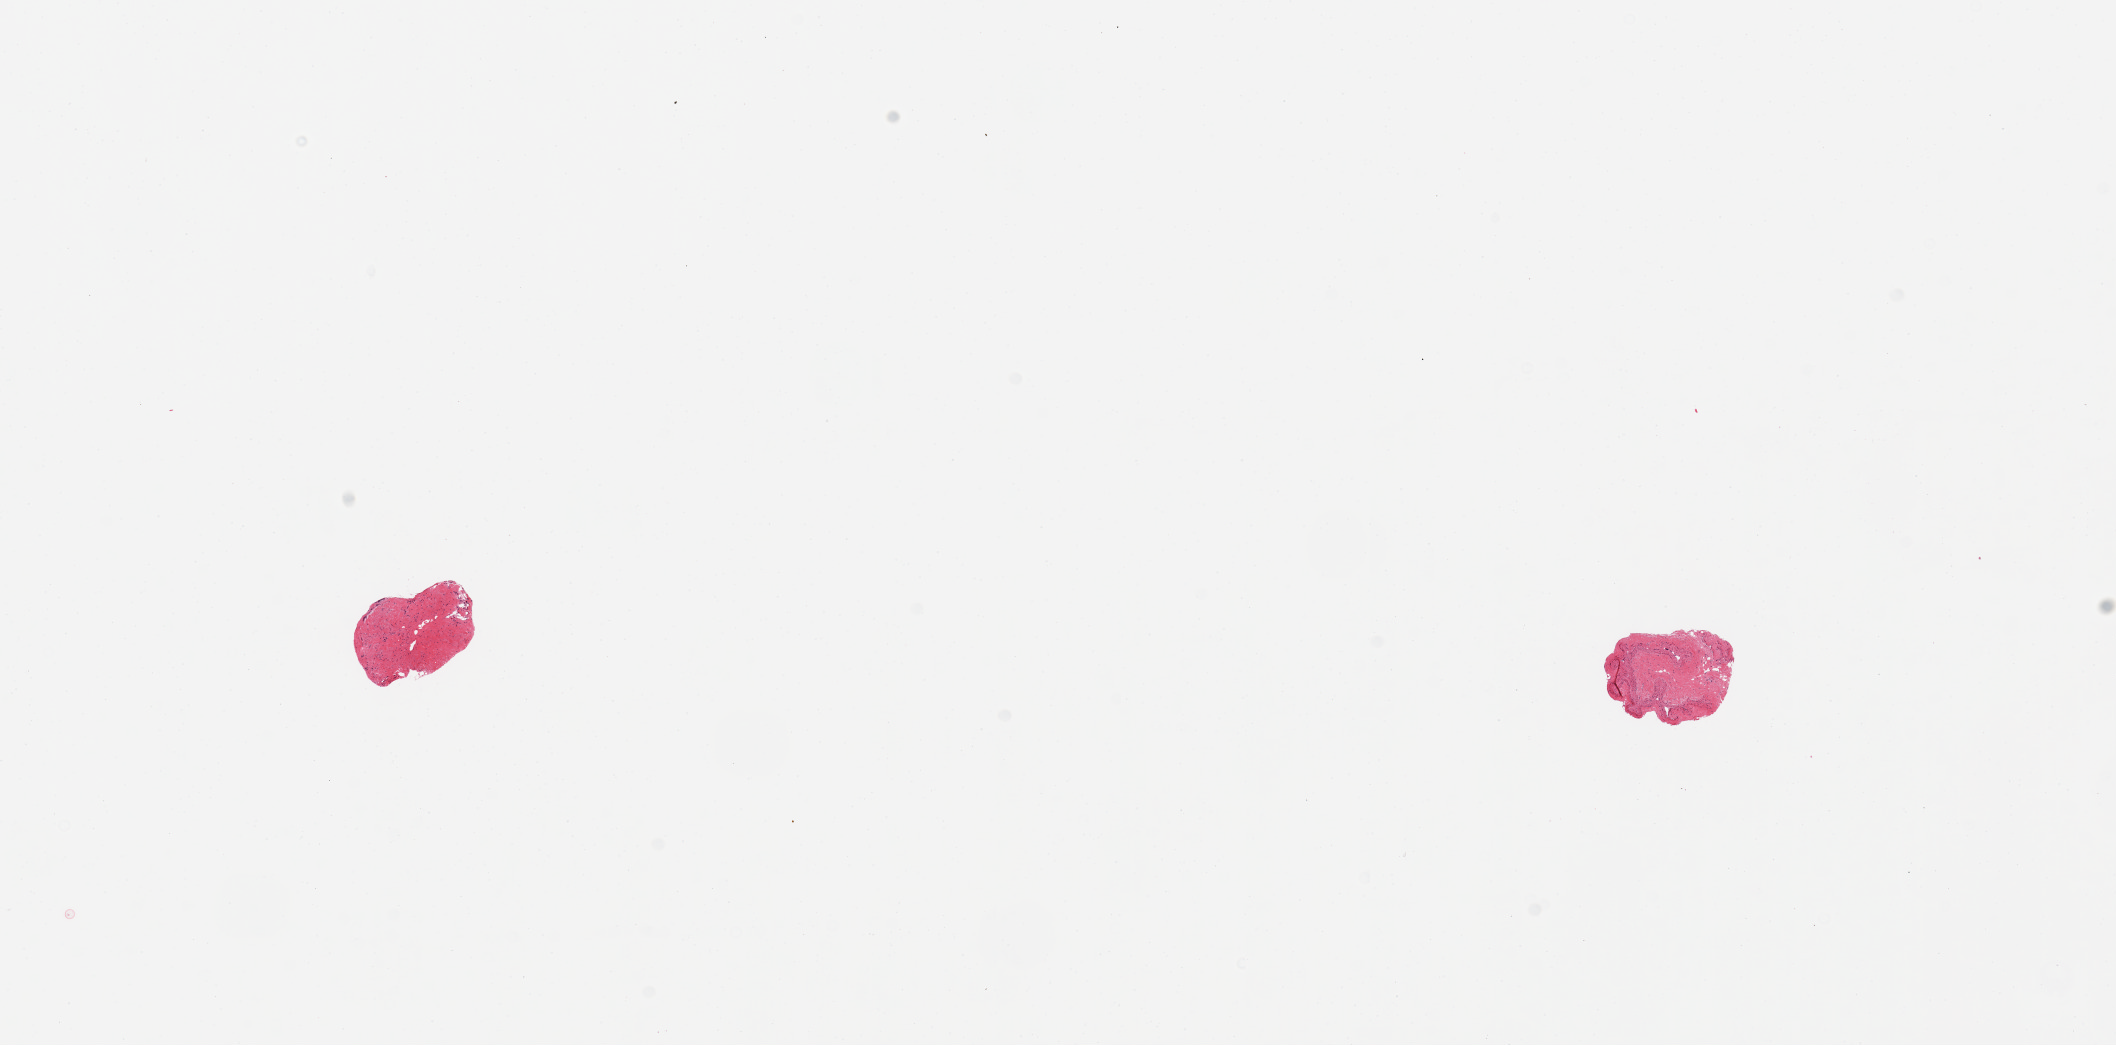
Digitized haematoxylin and eosin-stained section, brightfield, a low-resolution overview of the entire scanned area, about 16.7 x 8.3 mm (from a 20x scan). PAXgene-fixed paraffin-embedded (PFPE) section. Sampled site (target tissue): coronary artery. Donor tissue sample.
• pathologist's review note for this sample: 2 pieces; well trimmed; small